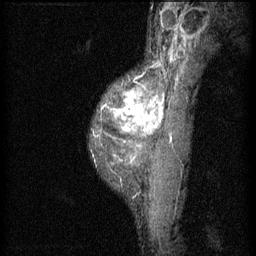
Breast MRI (dynamic contrast-enhanced), one sagittal slice; slice 45 of 60 in the series (ordered by position); 3 images stored at this slice position (order not interpretable as contrast timing); 1.5 T; TE 4.2 ms, TR 11 ms; 256 × 256 image matrix. Female patient, age 40 years.
Outlined on this slice (semi-automatically segmented with operator editing):
- analysis volume of interest (the breast-tissue region the enhancement analysis was run in; not a lesion): bounding box <92,48,171,195> (left, top, right, bottom; pixels)
- tumour enhancement mask (voxels above the 70 % enhancement threshold inside the analysis volume of interest): <103,90,165,133>